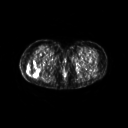
FDG PET of an extremity soft-tissue mass (from a PET/CT study), one axial slice; position 27 of 267 along the scan axis; 3.27 mm slice thickness; 128 × 128 image matrix, field of view 600 × 600 mm. Female patient, age 57 years. Case-level facts recorded for this patient, not image findings: histological type: epithelioid sarcoma with vascular differentiation; site of the primary tumour: right buttock.
Annotated regions visible in this slice (expert contour drawn on MRI and transferred to this co-registered scan by the dataset authors):
- gross tumour volume (mass): box from (x=26, y=60) to (x=38, y=76) px